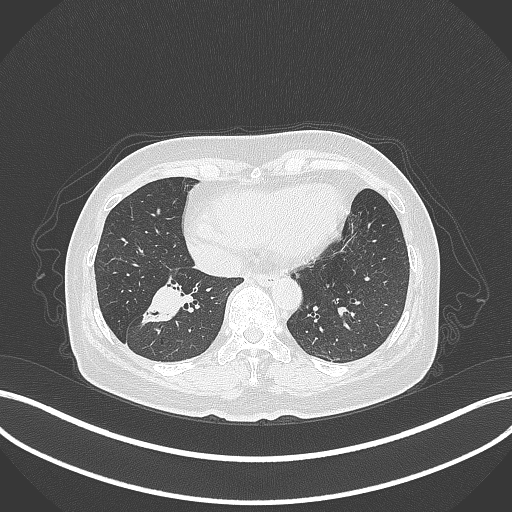
Chest CT, one axial slice; position 123 of 429 along the scan axis; lung window (W 1500 / L -600 HU); 1 mm slice thickness; 512 × 512 image matrix, field of view 400 × 400 mm. Patient: female, 67 years. Case-level facts recorded for this patient, not image findings: clinical TNM (as recorded): T1c N1 M0.
Outlined on this slice (bounding box drawn by a radiologist):
- lung tumour (recorded histology: adenocarcinoma): bounding box (x1, y1, x2, y2) in pixels: (142, 281, 192, 329)